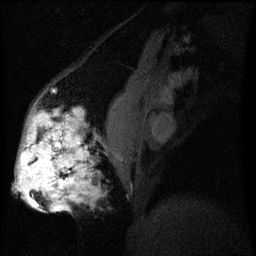
Breast MRI (dynamic contrast-enhanced), one sagittal slice; slice 23 of 60 in the series (ordered by position); dynamic contrast-enhanced series, image 2 of 3 at this slice position (ordered by acquisition); 1.5 T; TE 4.2 ms, TR 8 ms; 2.2 mm slice thickness; 256 × 256 image matrix. Female patient, age 50 years.
Annotated regions visible in this slice (semi-automatic segmentation, software-assisted and operator-edited):
- analysis volume of interest (the breast-tissue region the enhancement analysis was run in; not a lesion): box from (x=19, y=112) to (x=94, y=211) px
- tumour enhancement mask (voxels above the 70 % enhancement threshold inside the analysis volume of interest): (x=19, y=114)–(x=86, y=211)